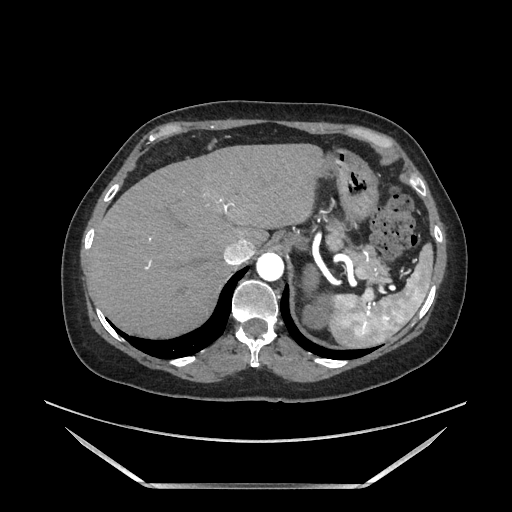
Contrast-enhanced abdominal CT, one axial slice. Position 146 of 205 along the scan axis. Soft-tissue window (W 400 / L 40 HU). 1.25 mm slice thickness. 512 × 512 image matrix. Female patient. From the clinical record (not read from this slice): diagnosis: adrenocortical carcinoma; tumour side: left adrenal; tumour size at pathology: 12.5 cm; Ki-67 index: 39 %; stage (as recorded): 3.
Structures marked on this image (semi-automatic segmentation, software-assisted and operator-edited):
- mass: bounding box <306,266,331,327> (left, top, right, bottom; pixels)